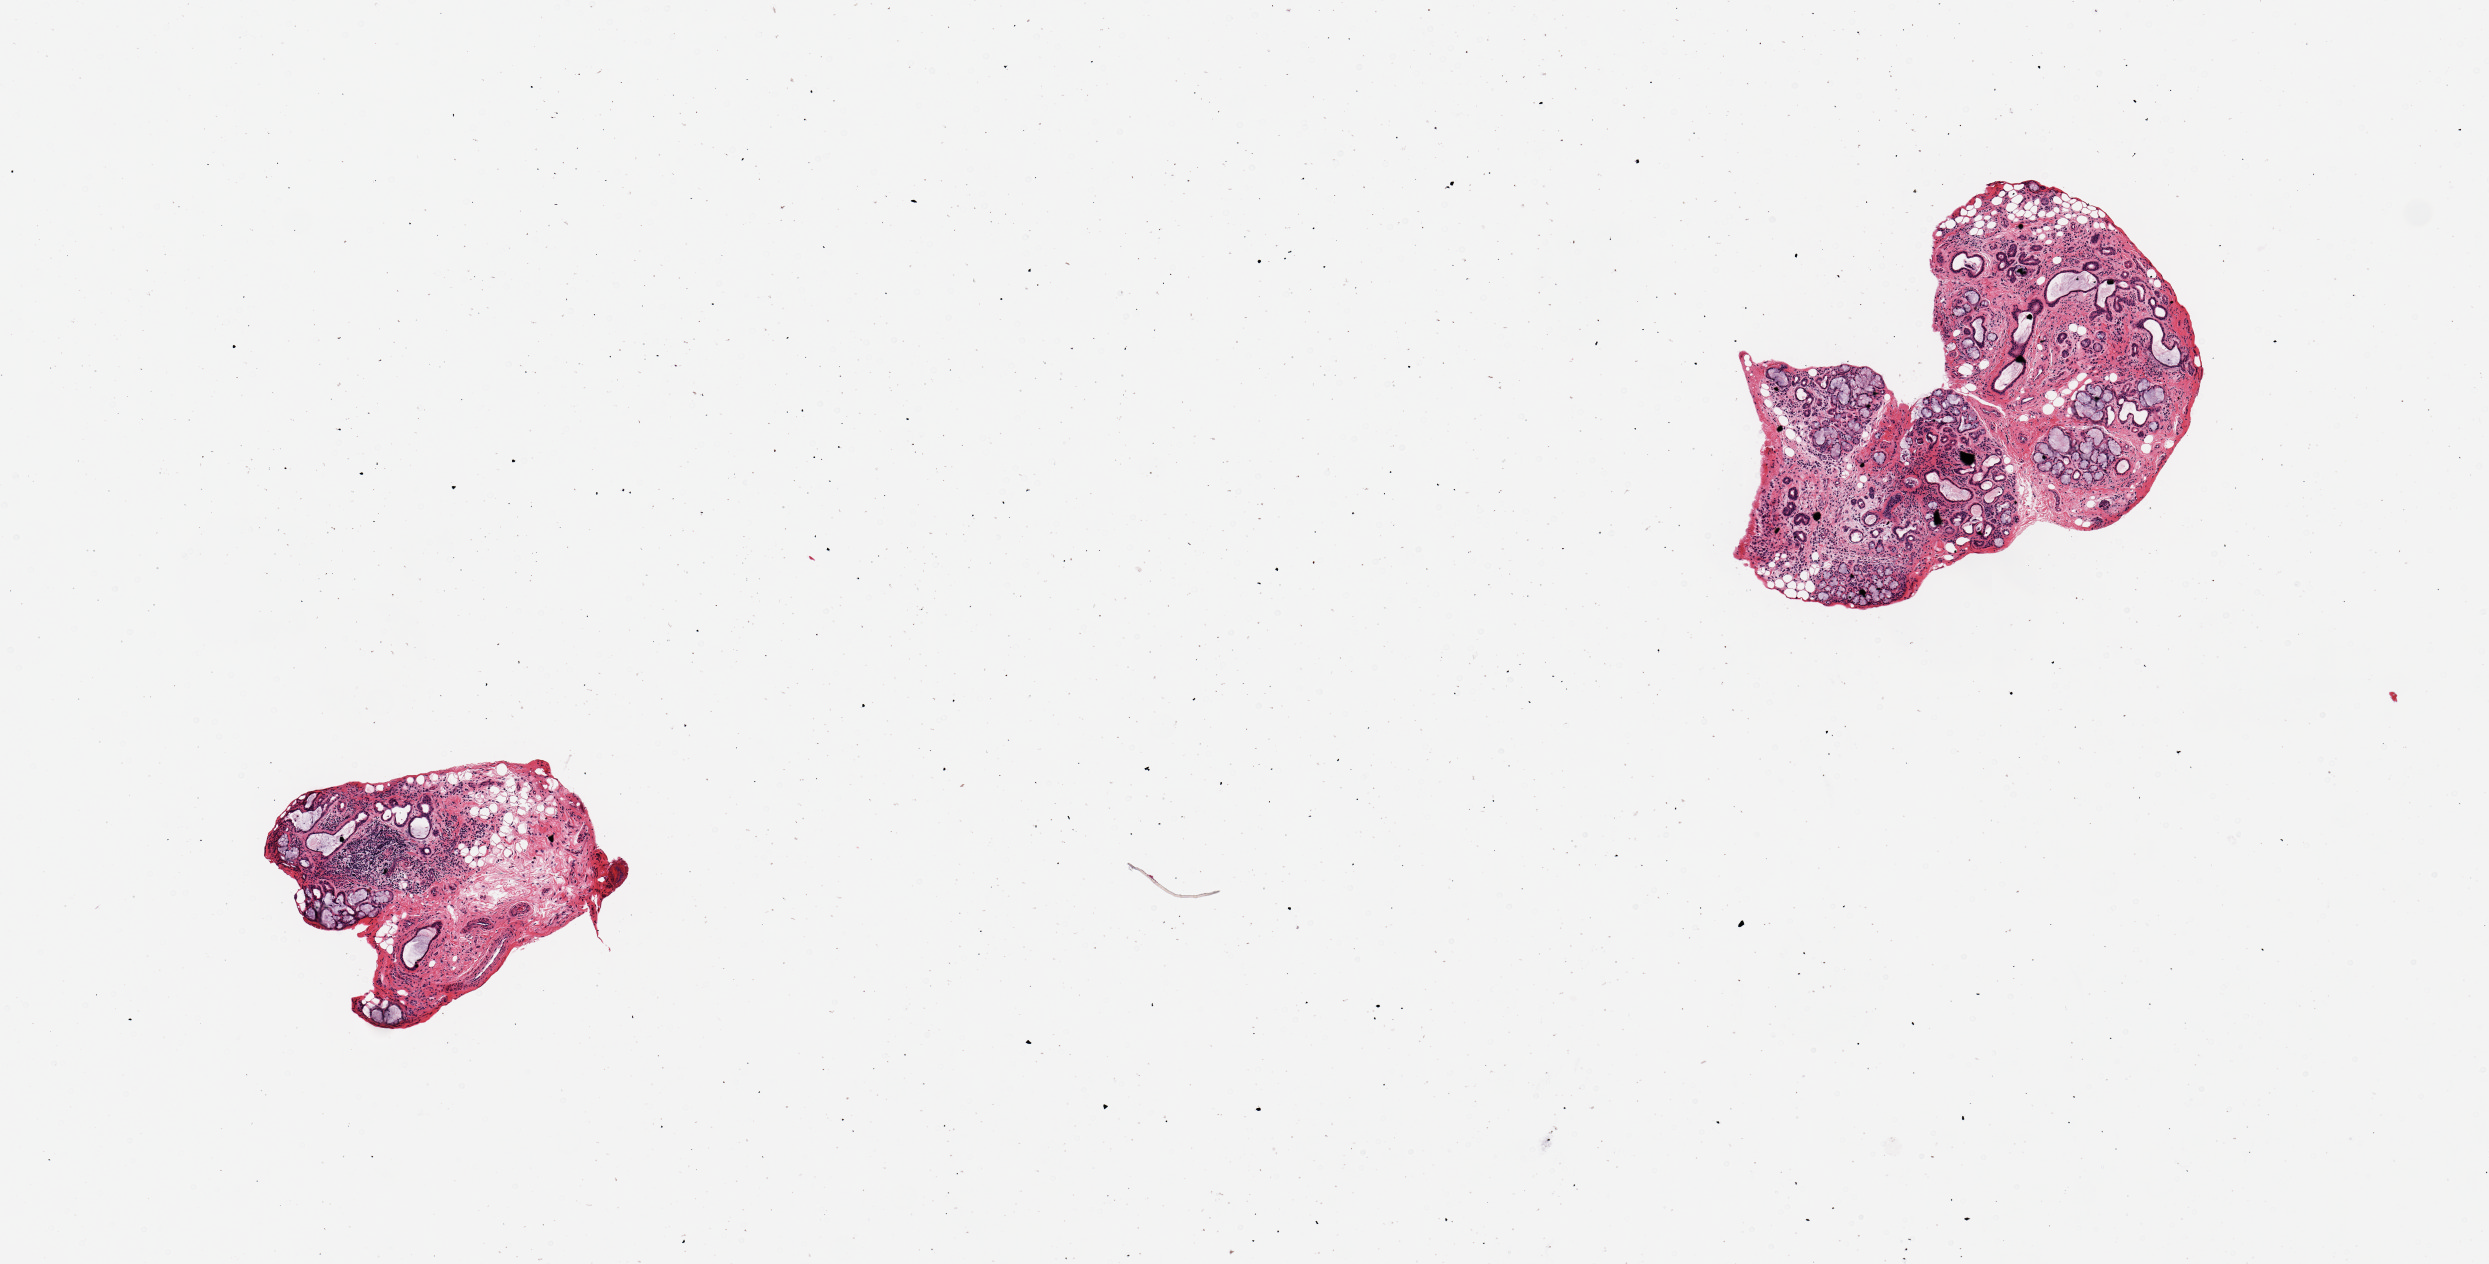
Hematoxylin and eosin (H&E) whole-slide image, low-resolution overview of the scanned area, about 9.8 x 5.0 mm, PAXgene-fixed paraffin-embedded (PFPE) section, sampled site (target tissue): minor salivary gland, tissue donor sample. Donor: female.
Pathologist's review note for this sample: 2 pieces, 60% glandular parenchyma/ductal elements. Fibrosis/chronic inflammation/sialadenitis.